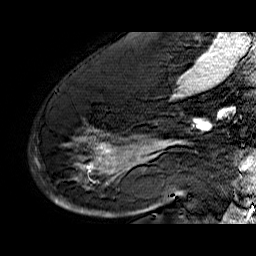
Breast MRI (dynamic contrast-enhanced), one sagittal slice; position 37 of 60 along the scan axis; dynamic contrast-enhanced series, time point 2 of 6 at this slice position (early post-contrast); 1.5 T; TE 6.4 ms, TR 32.9 ms; 256 × 256 image matrix, field of view 200 × 200 mm. Female patient. From the clinical record (not read from this slice): setting: breast cancer imaged before/during neoadjuvant chemotherapy; receptor status: HR-positive, HER2-negative.
Structures marked on this image (semi-automatic segmentation, software-assisted and operator-edited):
- analysis volume of interest (the breast-tissue region the enhancement analysis was run in; not a lesion): box from (x=52, y=74) to (x=176, y=210) px
- tumour enhancement mask (voxels above the 100 % enhancement threshold inside the analysis volume of interest): (x=55, y=138)–(x=172, y=203)